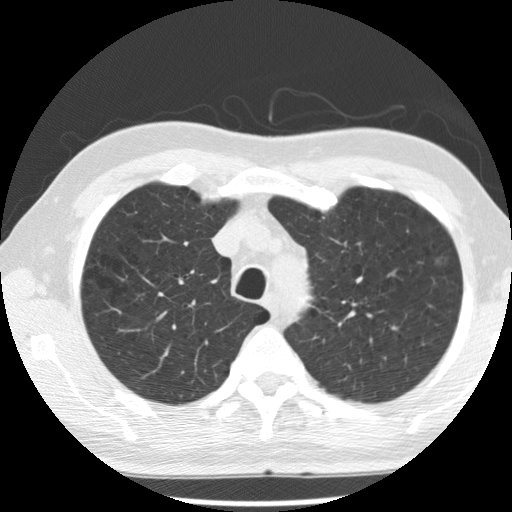
Chest CT (low-dose screening protocol), one axial image. First (baseline) screen. Lung window (W 1500 / L -600 HU). Slice 60 of 277 in the series. Male participant, aged 68 years at enrolment.
Lesion marked by an expert reader, box from (x=428, y=248) to (x=463, y=280) px. Screening reader's record for this exam (one nodule recorded; not confirmed to be the boxed lesion): non-calcified nodule or mass ≥4 mm, left upper lobe, 5 × 5 mm, poorly defined margins, ground glass attenuation. Official screen result: positive, change unspecified: nodule(s) >= 4 mm or enlarging nodule(s), mass(es), or other non-specific abnormalities suspicious for lung cancer. Later outcome: lung cancer diagnosed 648 days after this screen (after the second annual screen) — bronchiolo-alveolar adenocarcinoma, NOS, left upper lobe, moderately differentiated (G2), stage IA (AJCC 6th edition), 17 mm at pathology.